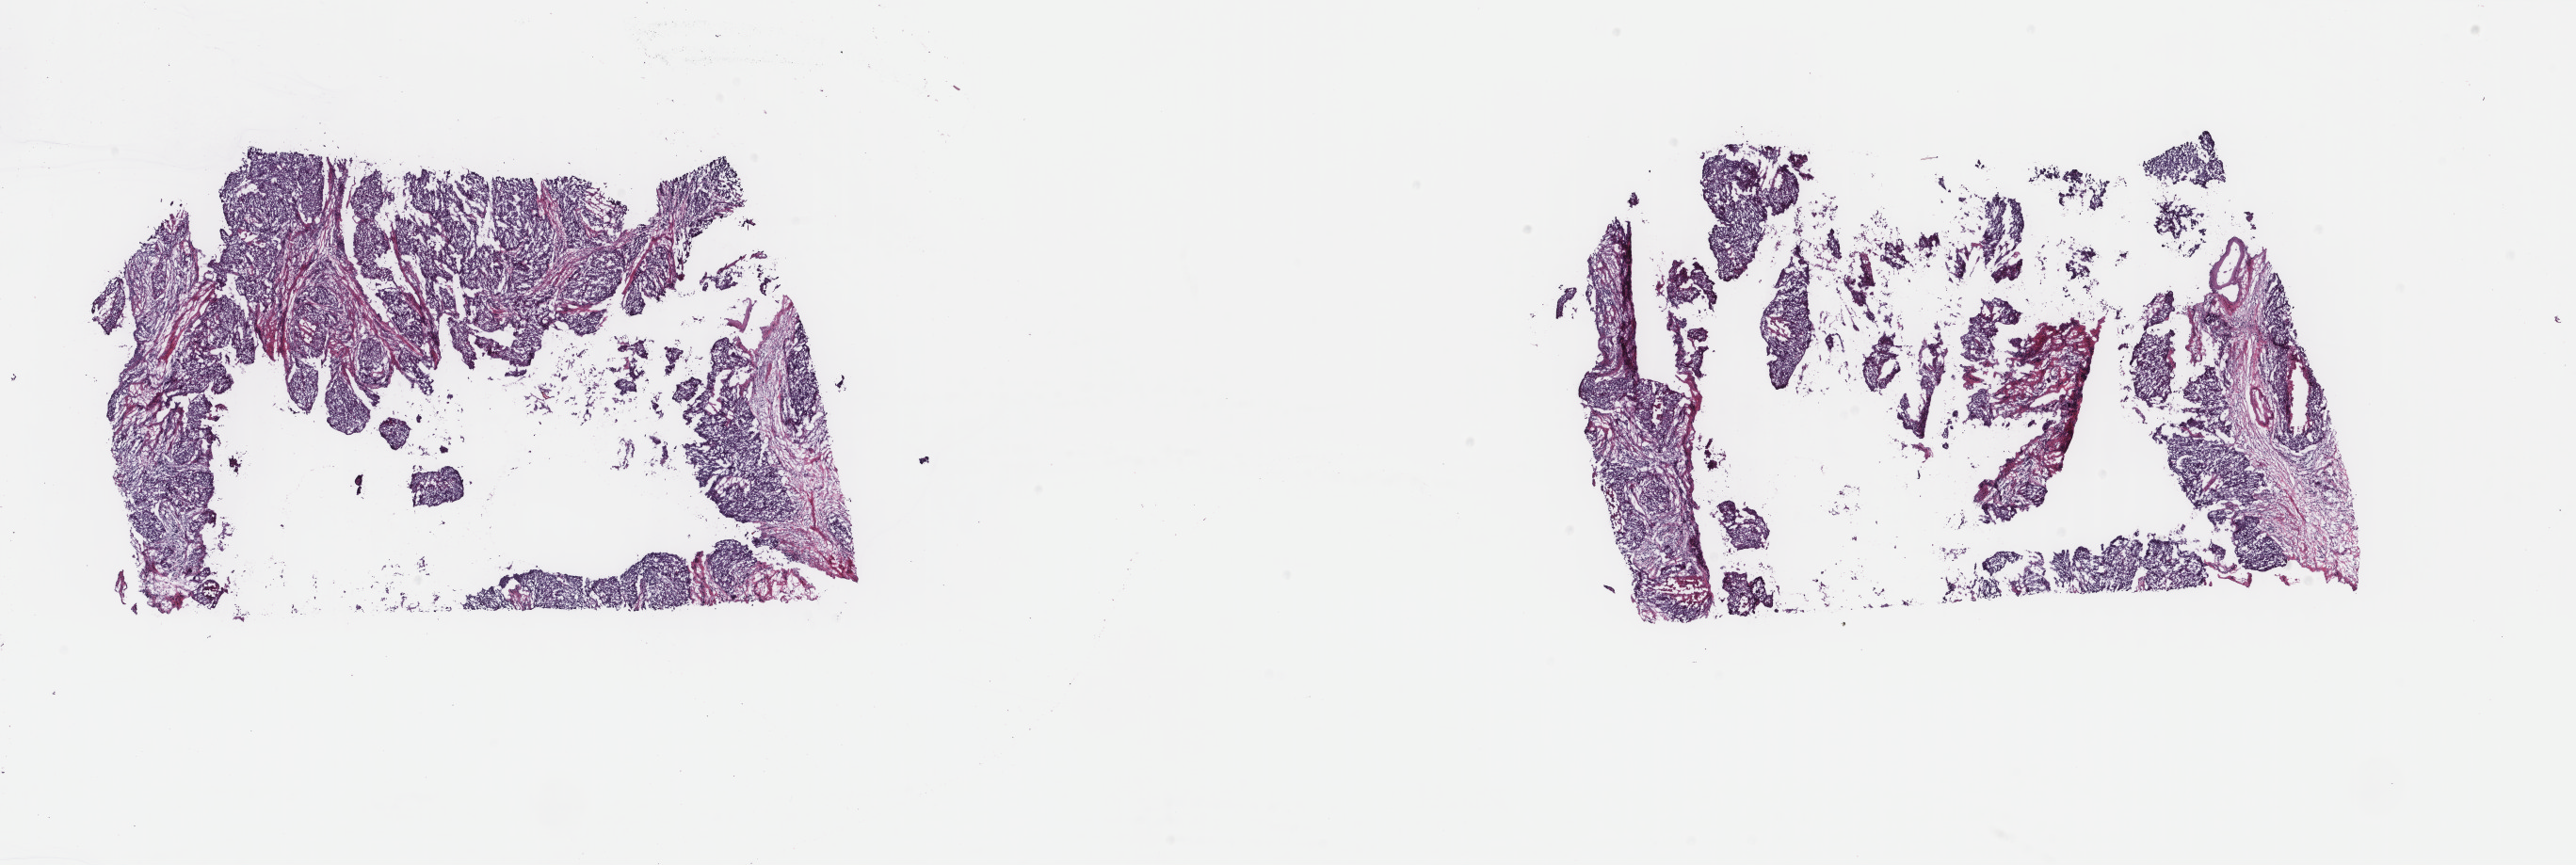
Digitized H&E tissue section (whole slide), shown as a low-resolution overview of the whole scanned area (about 21.7 x 7.3 mm, from a 40x scan); frozen section; primary tumour sample from the cervix. Patient: female, age at initial diagnosis 77 years. Histologic grade: G3 (poorly differentiated). Pathologist review of this section (percent, as recorded): tumour cells 70%, tumour nuclei 70%, normal cells 0%, stromal cells 20%, necrosis 10%. Infiltration values recorded for this section: lymphocyte infiltration 40%, monocyte infiltration 10%, neutrophil infiltration 40%.
* FIGO stage: IB
* diagnosis: Squamous cell carcinoma, NOS (cervix uteri)